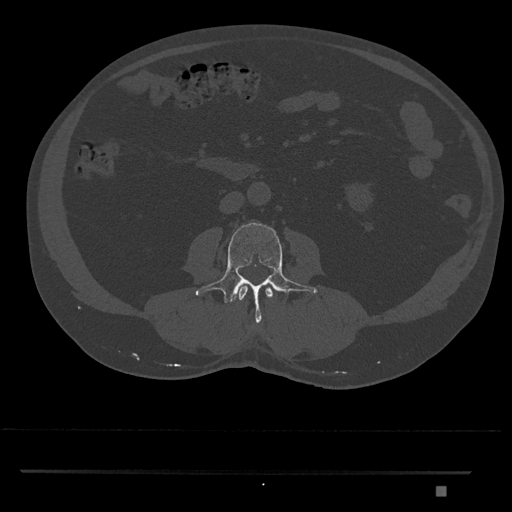
CT including the spine, one axial slice. Slice 691 of 1134 in the series (ordered by position). Reconstruction kernel Br40s/3. Bone window (W 1800 / L 400 HU). 512 × 512 image matrix, field of view 429 × 429 mm. Male patient, age 65 years. From the clinical record (not read from this slice): primary cancer: prostate.
Outlined on this slice (semi-automatic segmentation, software-assisted and operator-edited):
- L2 vertebra: bounding box <238,285,273,300> (left, top, right, bottom; pixels)
- L3 vertebra: <195,222,317,323>